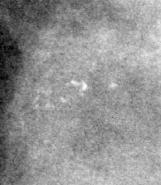
Crop from a digitized film mammogram around one marked abnormality; right breast; MLO view; BI-RADS breast density category 4 (scale 1–4).
Marked abnormality: calcifications, morphology pleomorphic, distribution clustered; BI-RADS assessment category 4; subtlety rating 3 on a 1 (subtle) to 5 (obvious) scale; pathology (as recorded): benign.